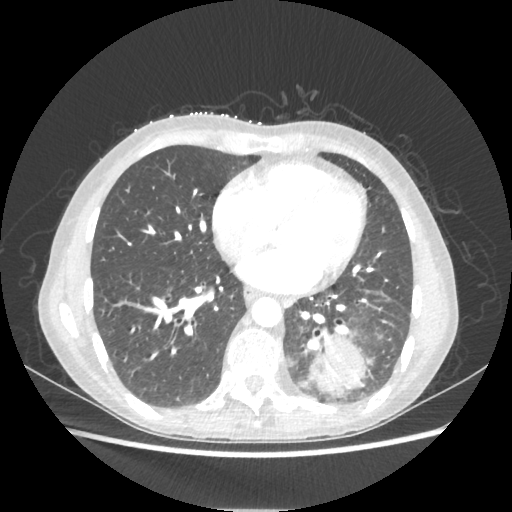
Chest CT, one axial slice. Slice 85 of 221 in the series (ordered by position). Reconstruction kernel STANDARD. Lung window (W 1500 / L -600 HU). 1.25 mm slice thickness. 512 × 512 image matrix, field of view 360 × 360 mm. Patient: female, 53 years. From the clinical record (not read from this slice): clinical TNM (as recorded): T3 N0 M0.
Annotated regions visible in this slice (bounding box drawn by a radiologist):
- lung tumour (recorded histology: adenocarcinoma): bounding box <310,337,368,393> (left, top, right, bottom; pixels)